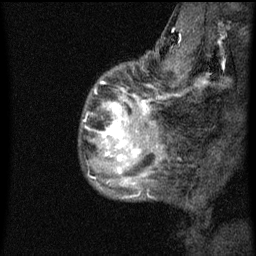
Breast MRI (dynamic contrast-enhanced), one sagittal slice. Position 13 of 60 along the scan axis. Dynamic contrast-enhanced series, image 2 of 3 at this slice position (ordered by acquisition). 1.5 T. TE 4.2 ms, TR 8 ms. 256 × 256 image matrix. Patient: female, 50 years.
Annotated regions visible in this slice (semi-automatically segmented with operator editing):
- analysis volume of interest (the breast-tissue region the enhancement analysis was run in; not a lesion): bounding box [x1, y1, x2, y2] px = [83, 72, 141, 187]
- tumour enhancement mask (voxels above the 70 % enhancement threshold inside the analysis volume of interest): [104, 102, 140, 161]